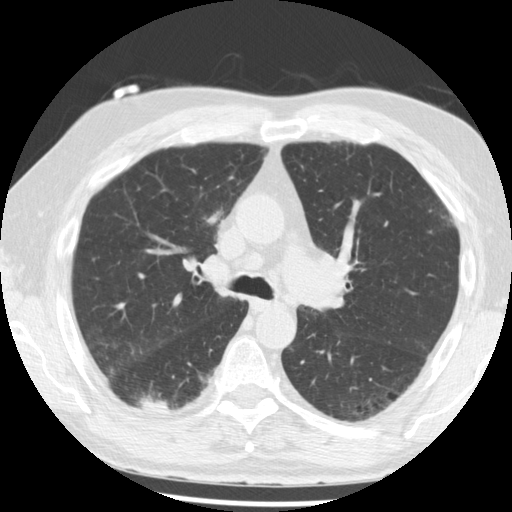
Low-dose screening chest CT, axial slice. Third screening round (two years after baseline). Lung window (W 1500 / L -600 HU). 2.5 mm slice thickness. Standard (soft-tissue) reconstruction kernel (STANDARD). Male participant, aged 68 years at enrolment. Current smoker at enrolment.
Expert-annotated lung lesion, box from (x=125, y=378) to (x=183, y=423) px. The screening reader recorded 3 non-calcified nodules or masses ≥4 mm on this exam (right lower lobe, right lower lobe, right lower lobe); which of them this box marks is not recorded. Official screen result: positive, other. Participant outcome: lung cancer diagnosed 48 days after this screen — squamous cell carcinoma, NOS, right lower lobe, moderately differentiated (G2), stage IB (AJCC 6th edition), 20 mm at pathology.